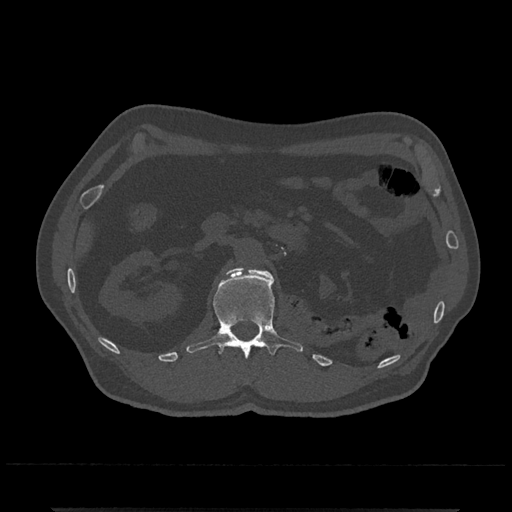
CT including the spine, one axial slice. Position 359 of 797 along the scan axis. Bone window (W 1800 / L 400 HU). 0.5 mm slice thickness. 512 × 512 image matrix, field of view 393 × 393 mm. Patient: male, 67 years. From the clinical record (not read from this slice): primary cancer: prostate.
Structures marked on this image (semi-automatic segmentation, software-assisted and operator-edited):
- L1 vertebra: bounding box (x1, y1, x2, y2) in pixels: (186, 267, 303, 359)